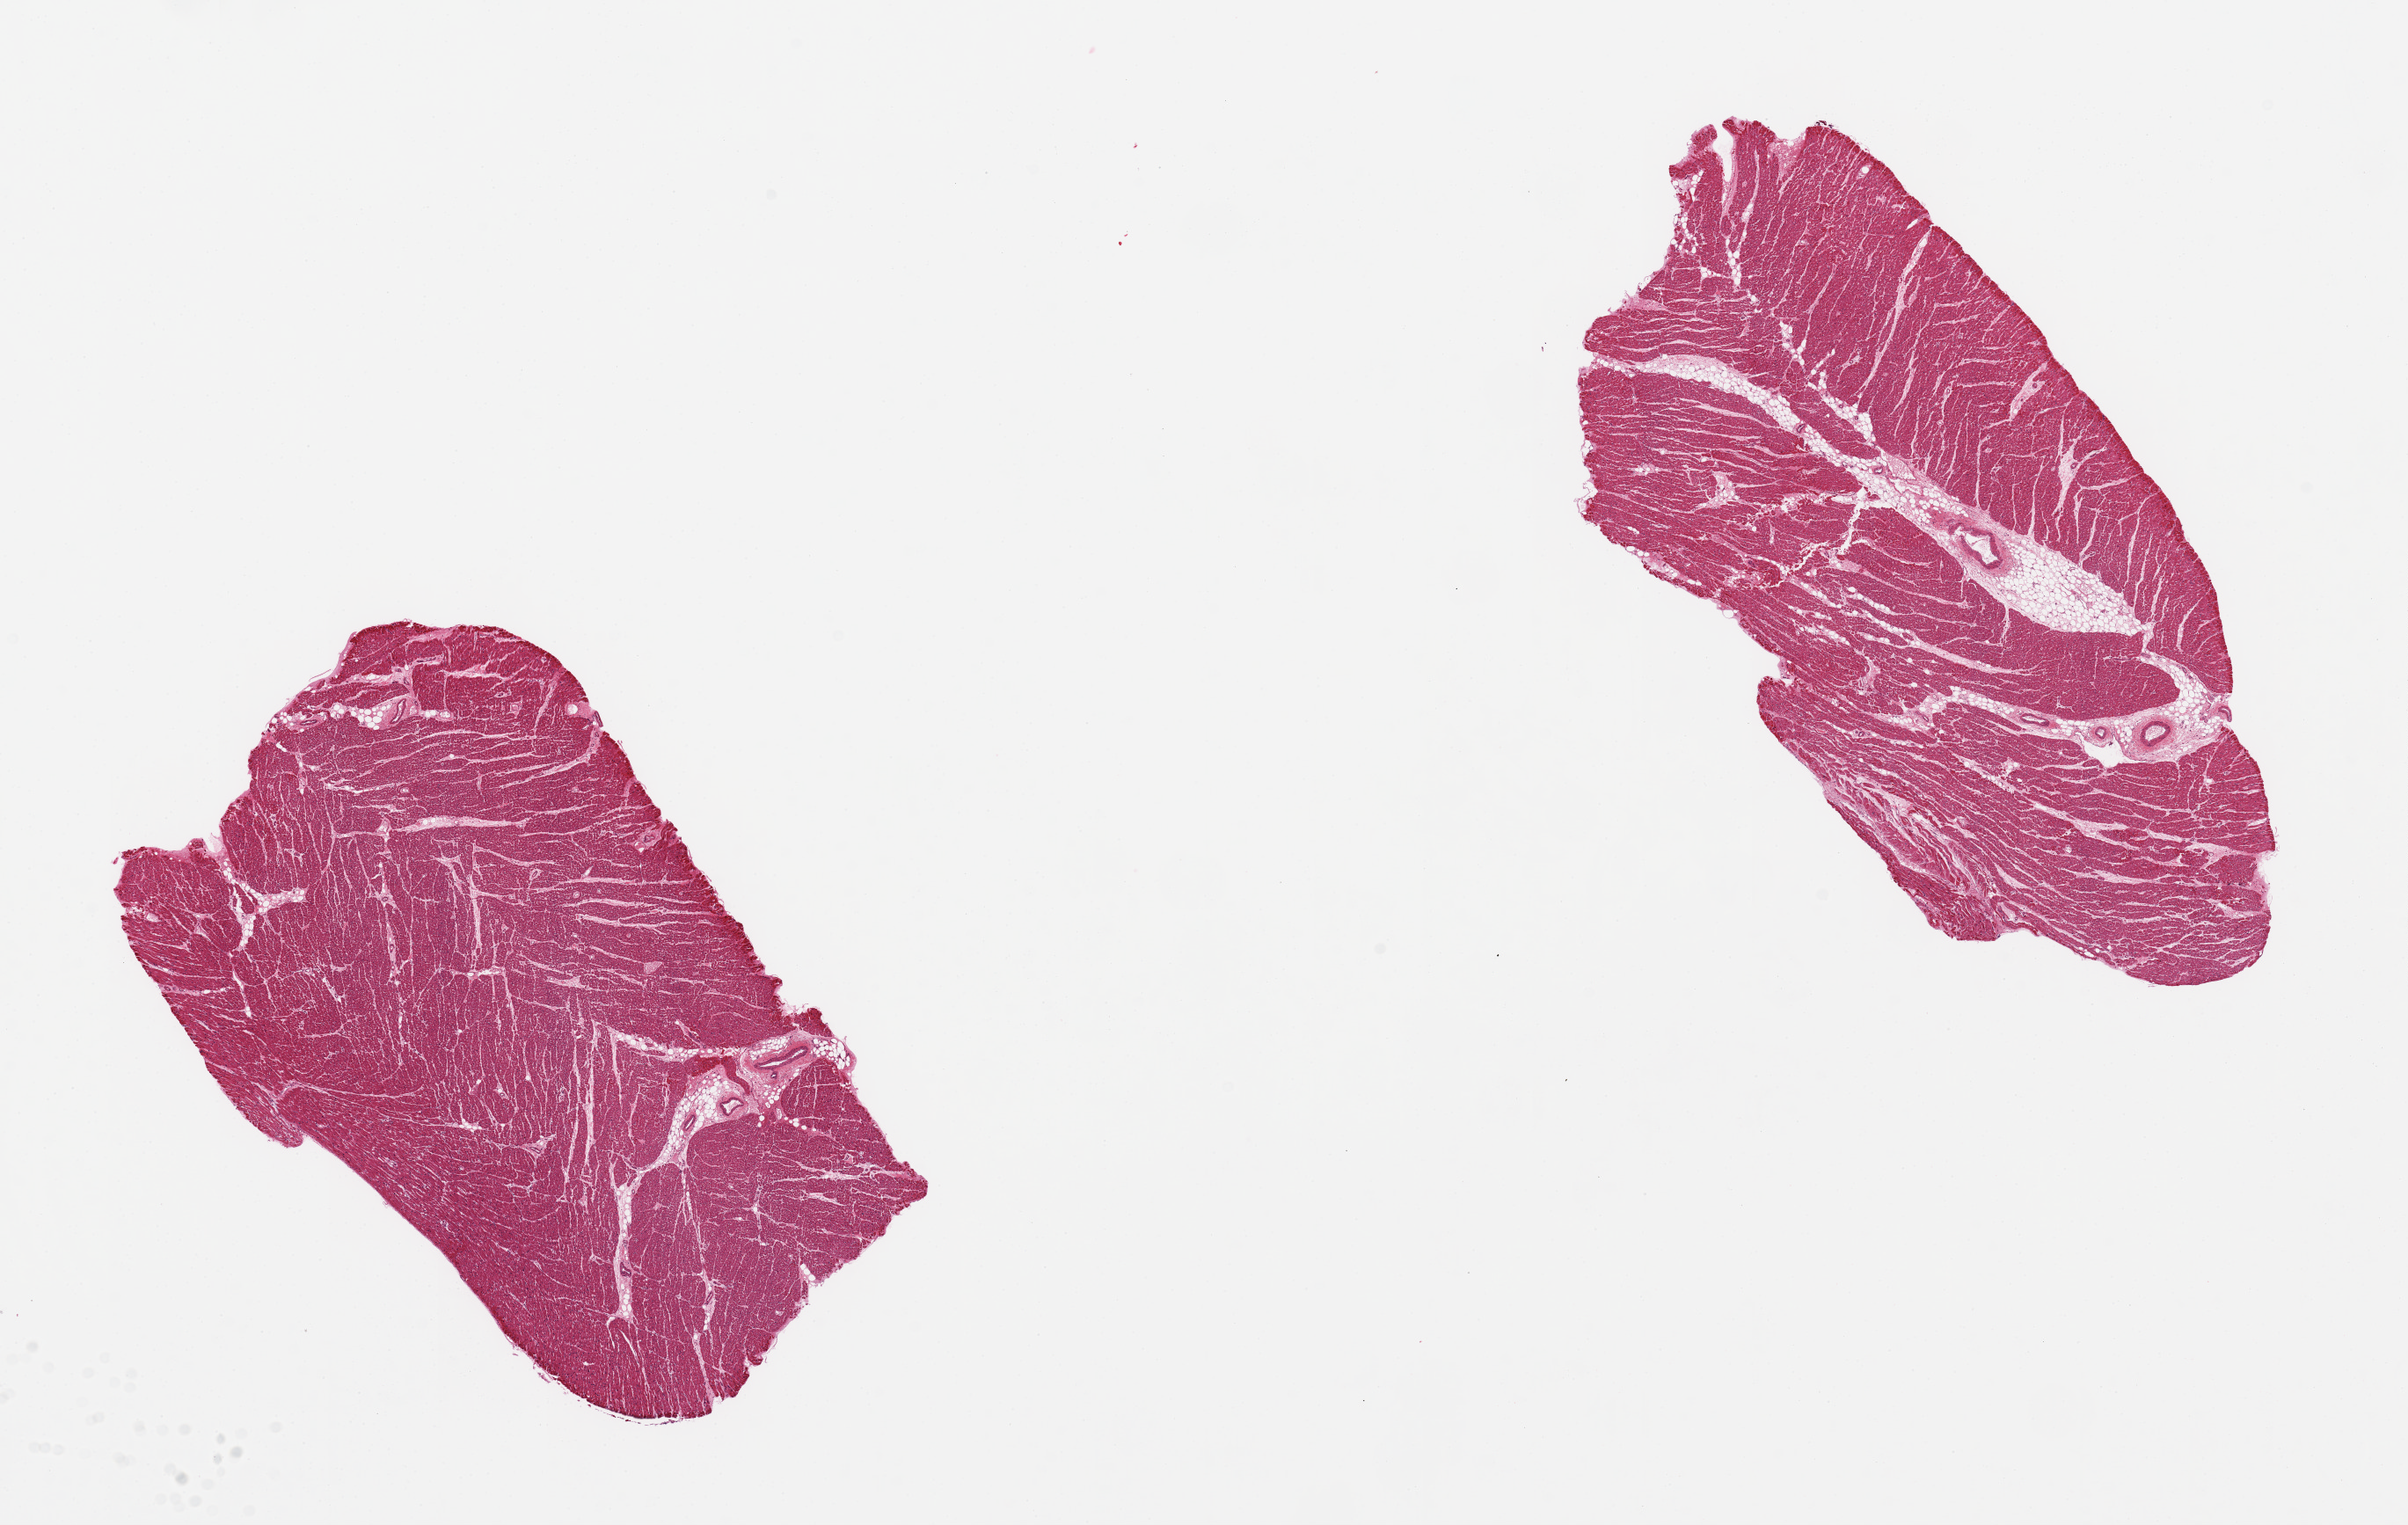
Whole-slide image, hematoxylin and eosin (H&E) stain, whole scanned area (about 21.7 x 13.7 mm, acquisition: 20x scan) shown as a low-resolution overview. PAXgene-fixed paraffin-embedded (PFPE) section. Target tissue: heart. Tissue donor sample. Donor: female.
Pathologist's review note for this sample: 2 pieces, no significant ischemic changes.